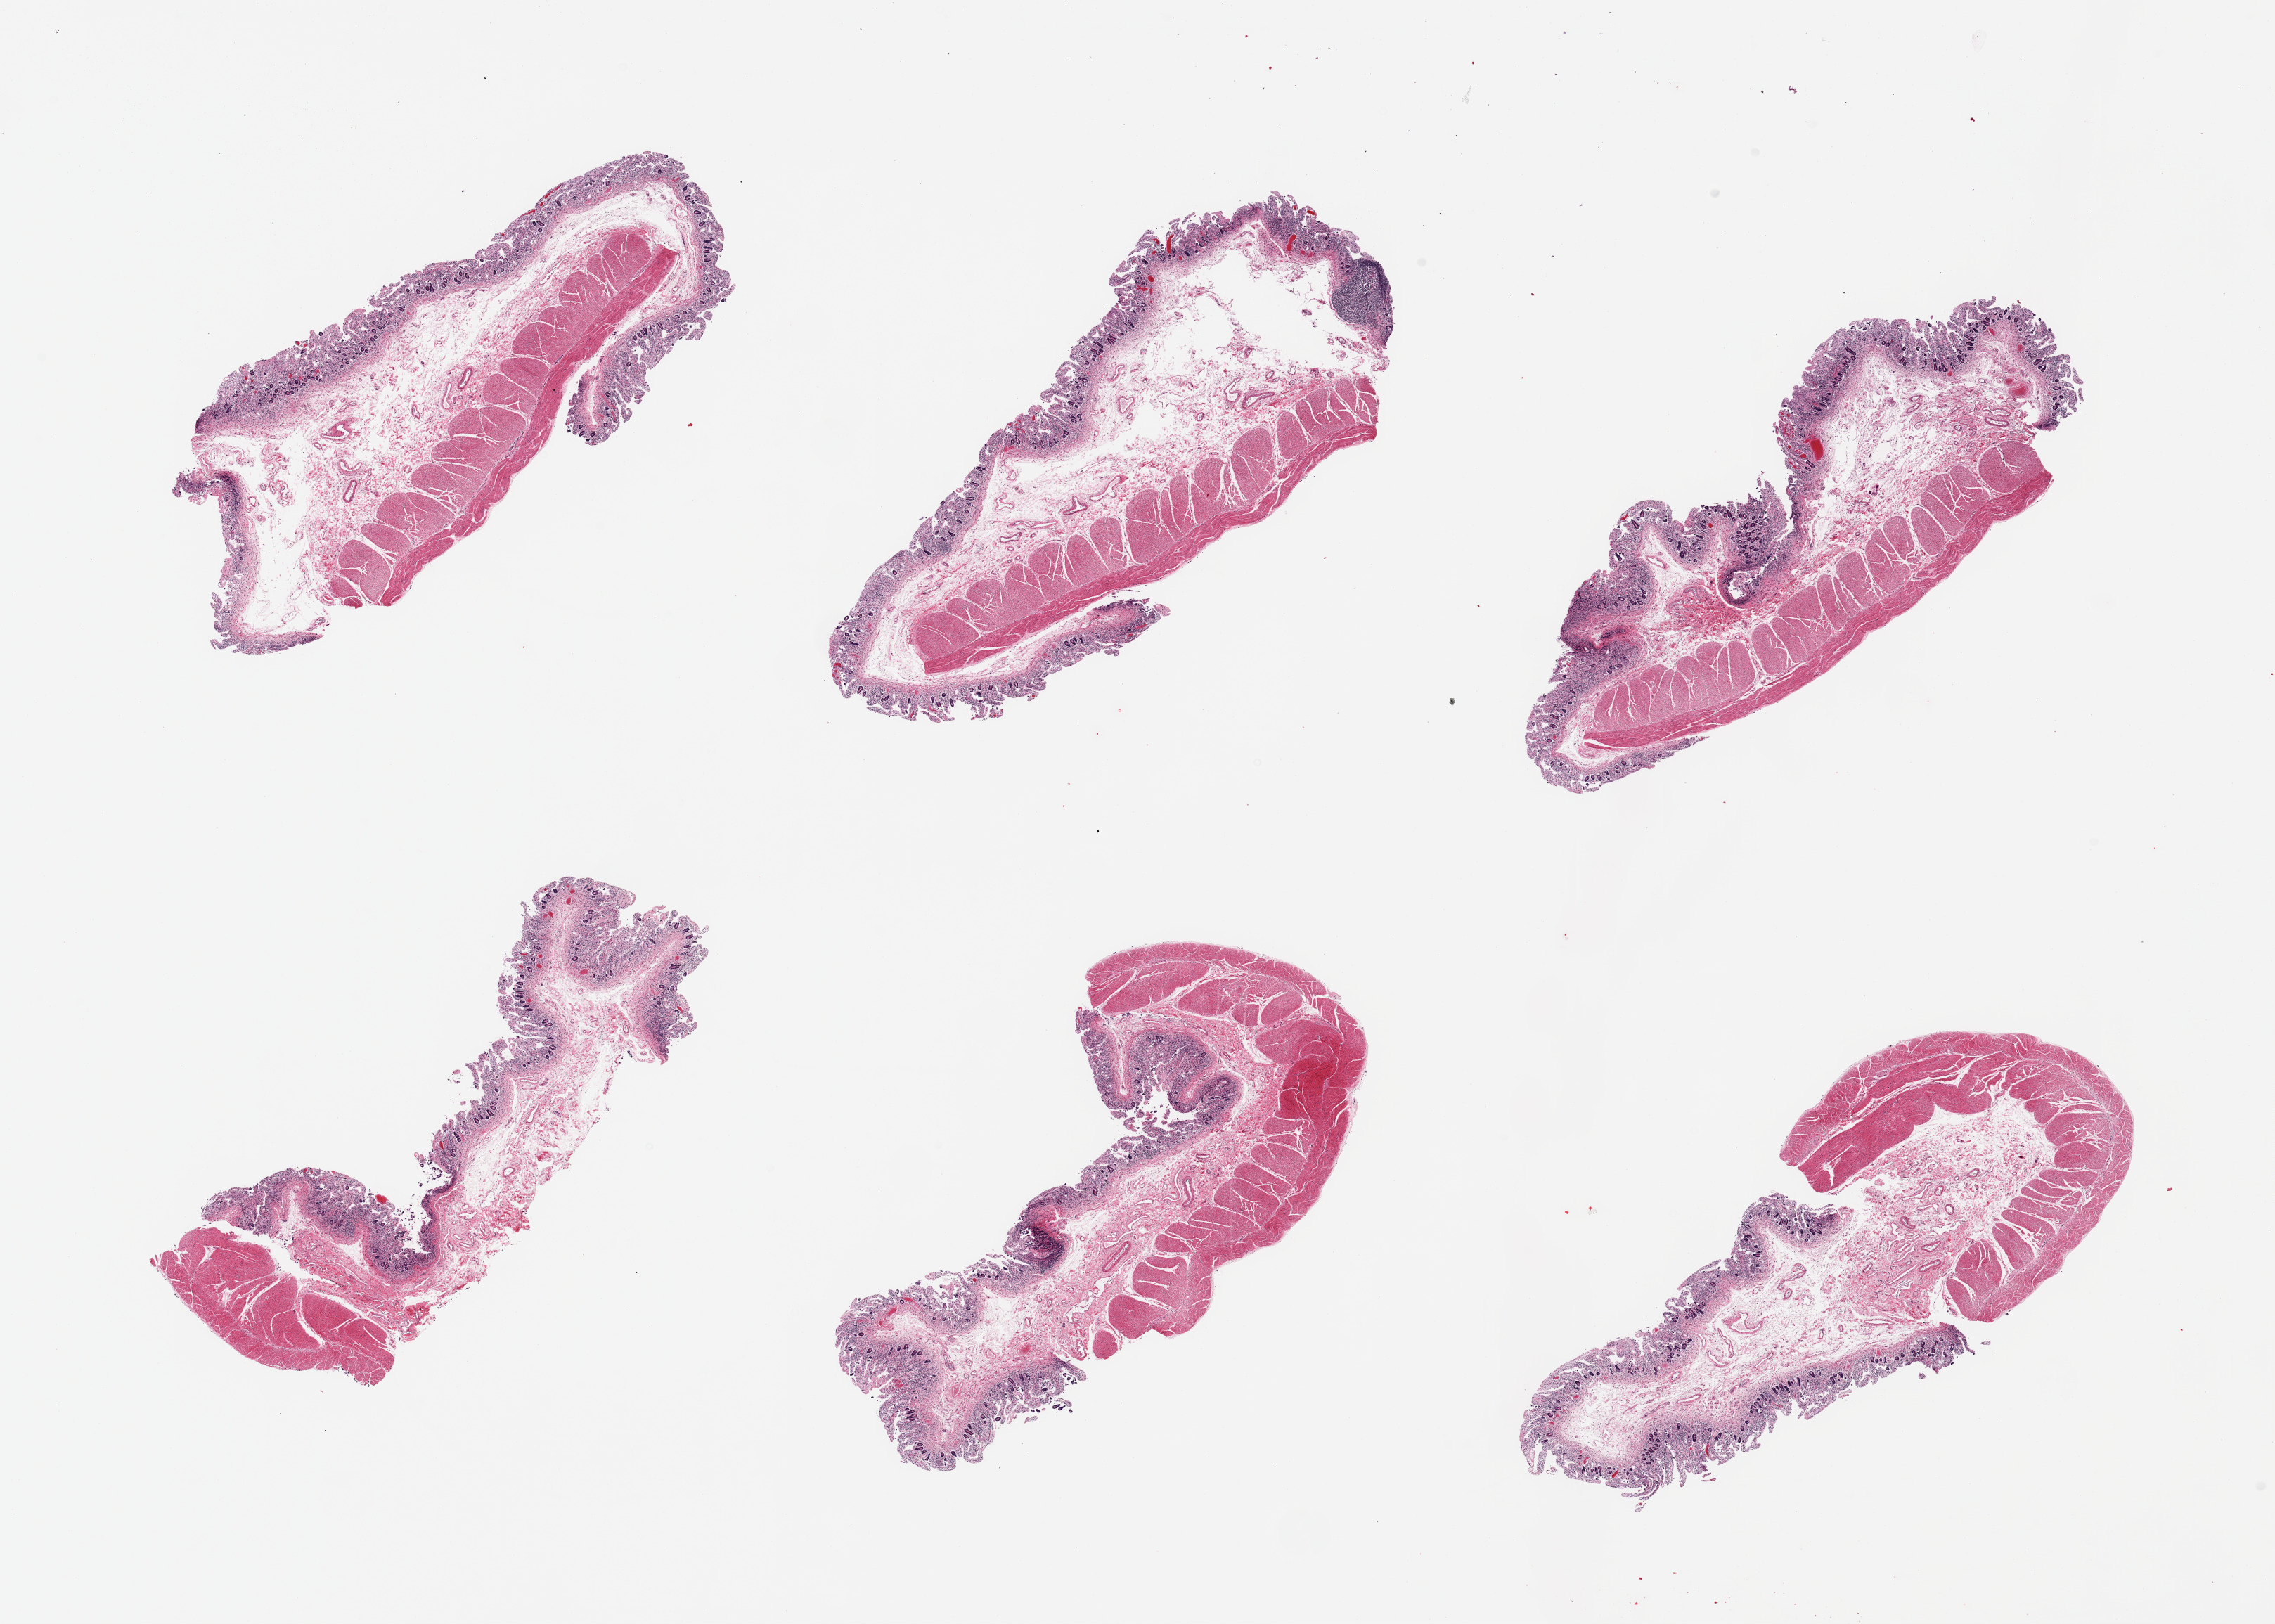
Whole-slide image, haematoxylin and eosin stain — low-resolution overview of the scanned area, about 25.6 x 18.3 mm (from a 20x scan); PAXgene-fixed, paraffin-embedded tissue; sampled site (target tissue): transverse colon; tissue donor sample. Donor sex: female.
• pathologist's review note for this sample: 6 pieces; mucosa severely autolyzed; muscularis slightly to moderately autolyzed